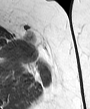
MRI of an extremity soft-tissue mass, one axial slice. Slice 28 of 45 in the series (ordered by position). MR volume resampled by the dataset authors to the PET/CT grid (not the native acquisition matrix). 3.27 mm slice thickness. 90 × 109 image matrix, field of view 88 × 106 mm. Female patient. From the clinical record (not read from this slice): histological type: leiomyosarcoma; grade: intermediate; site of the primary tumour: parascapusular.
Outlined on this slice (expert contour drawn on MRI and transferred to this co-registered scan by the dataset authors):
- gross tumour volume including surrounding oedema: bounding box [x1, y1, x2, y2] px = [23, 32, 40, 47]
- gross tumour volume (mass): [24, 32, 36, 45]